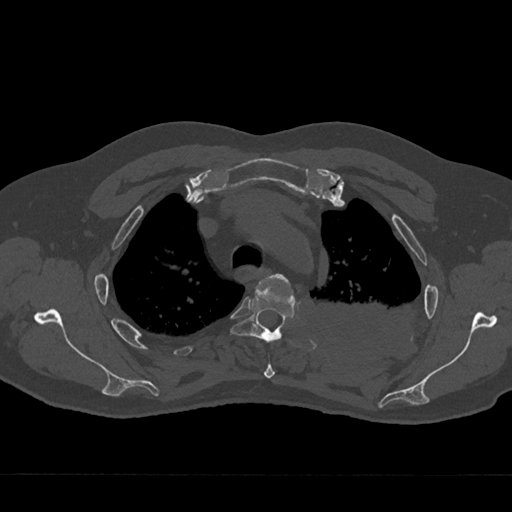
CT including the spine, one axial slice. Position 534 of 797 along the scan axis. Reconstruction kernel Br40s/3. 120 kVp. Bone window (W 1800 / L 400 HU). 0.5 mm slice thickness. 512 × 512 image matrix, field of view 377 × 377 mm. Patient: male, 75 years. Case-level facts recorded for this patient, not image findings: primary cancer: renal; vertebrae with lytic lesions (as recorded): T4.
Annotated regions visible in this slice (semi-automatically segmented with operator editing):
- T3 vertebra: bounding box [x1, y1, x2, y2] px = [263, 274, 291, 379]
- T4 vertebra: [230, 282, 296, 342]